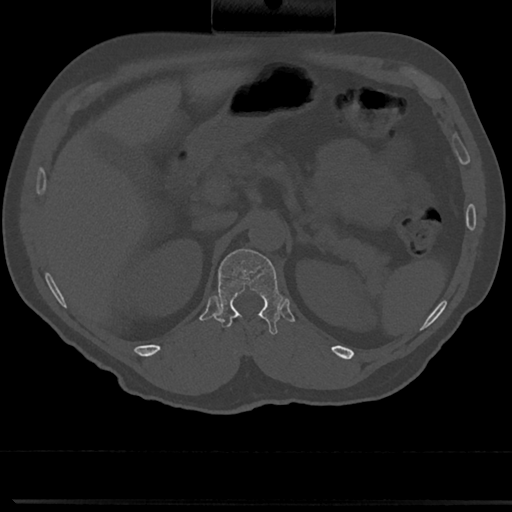
CT including the spine, one axial slice. Slice 151 of 817 in the series (ordered by position). Reconstruction kernel Br40s/3. Bone window (W 1800 / L 400 HU). 0.5 mm slice thickness. 512 × 512 image matrix. Male patient, age 61 years. From the clinical record (not read from this slice): primary cancer: prostate.
Outlined on this slice (semi-automatic segmentation, software-assisted and operator-edited):
- T12 vertebra: bounding box <214,246,279,332> (left, top, right, bottom; pixels)